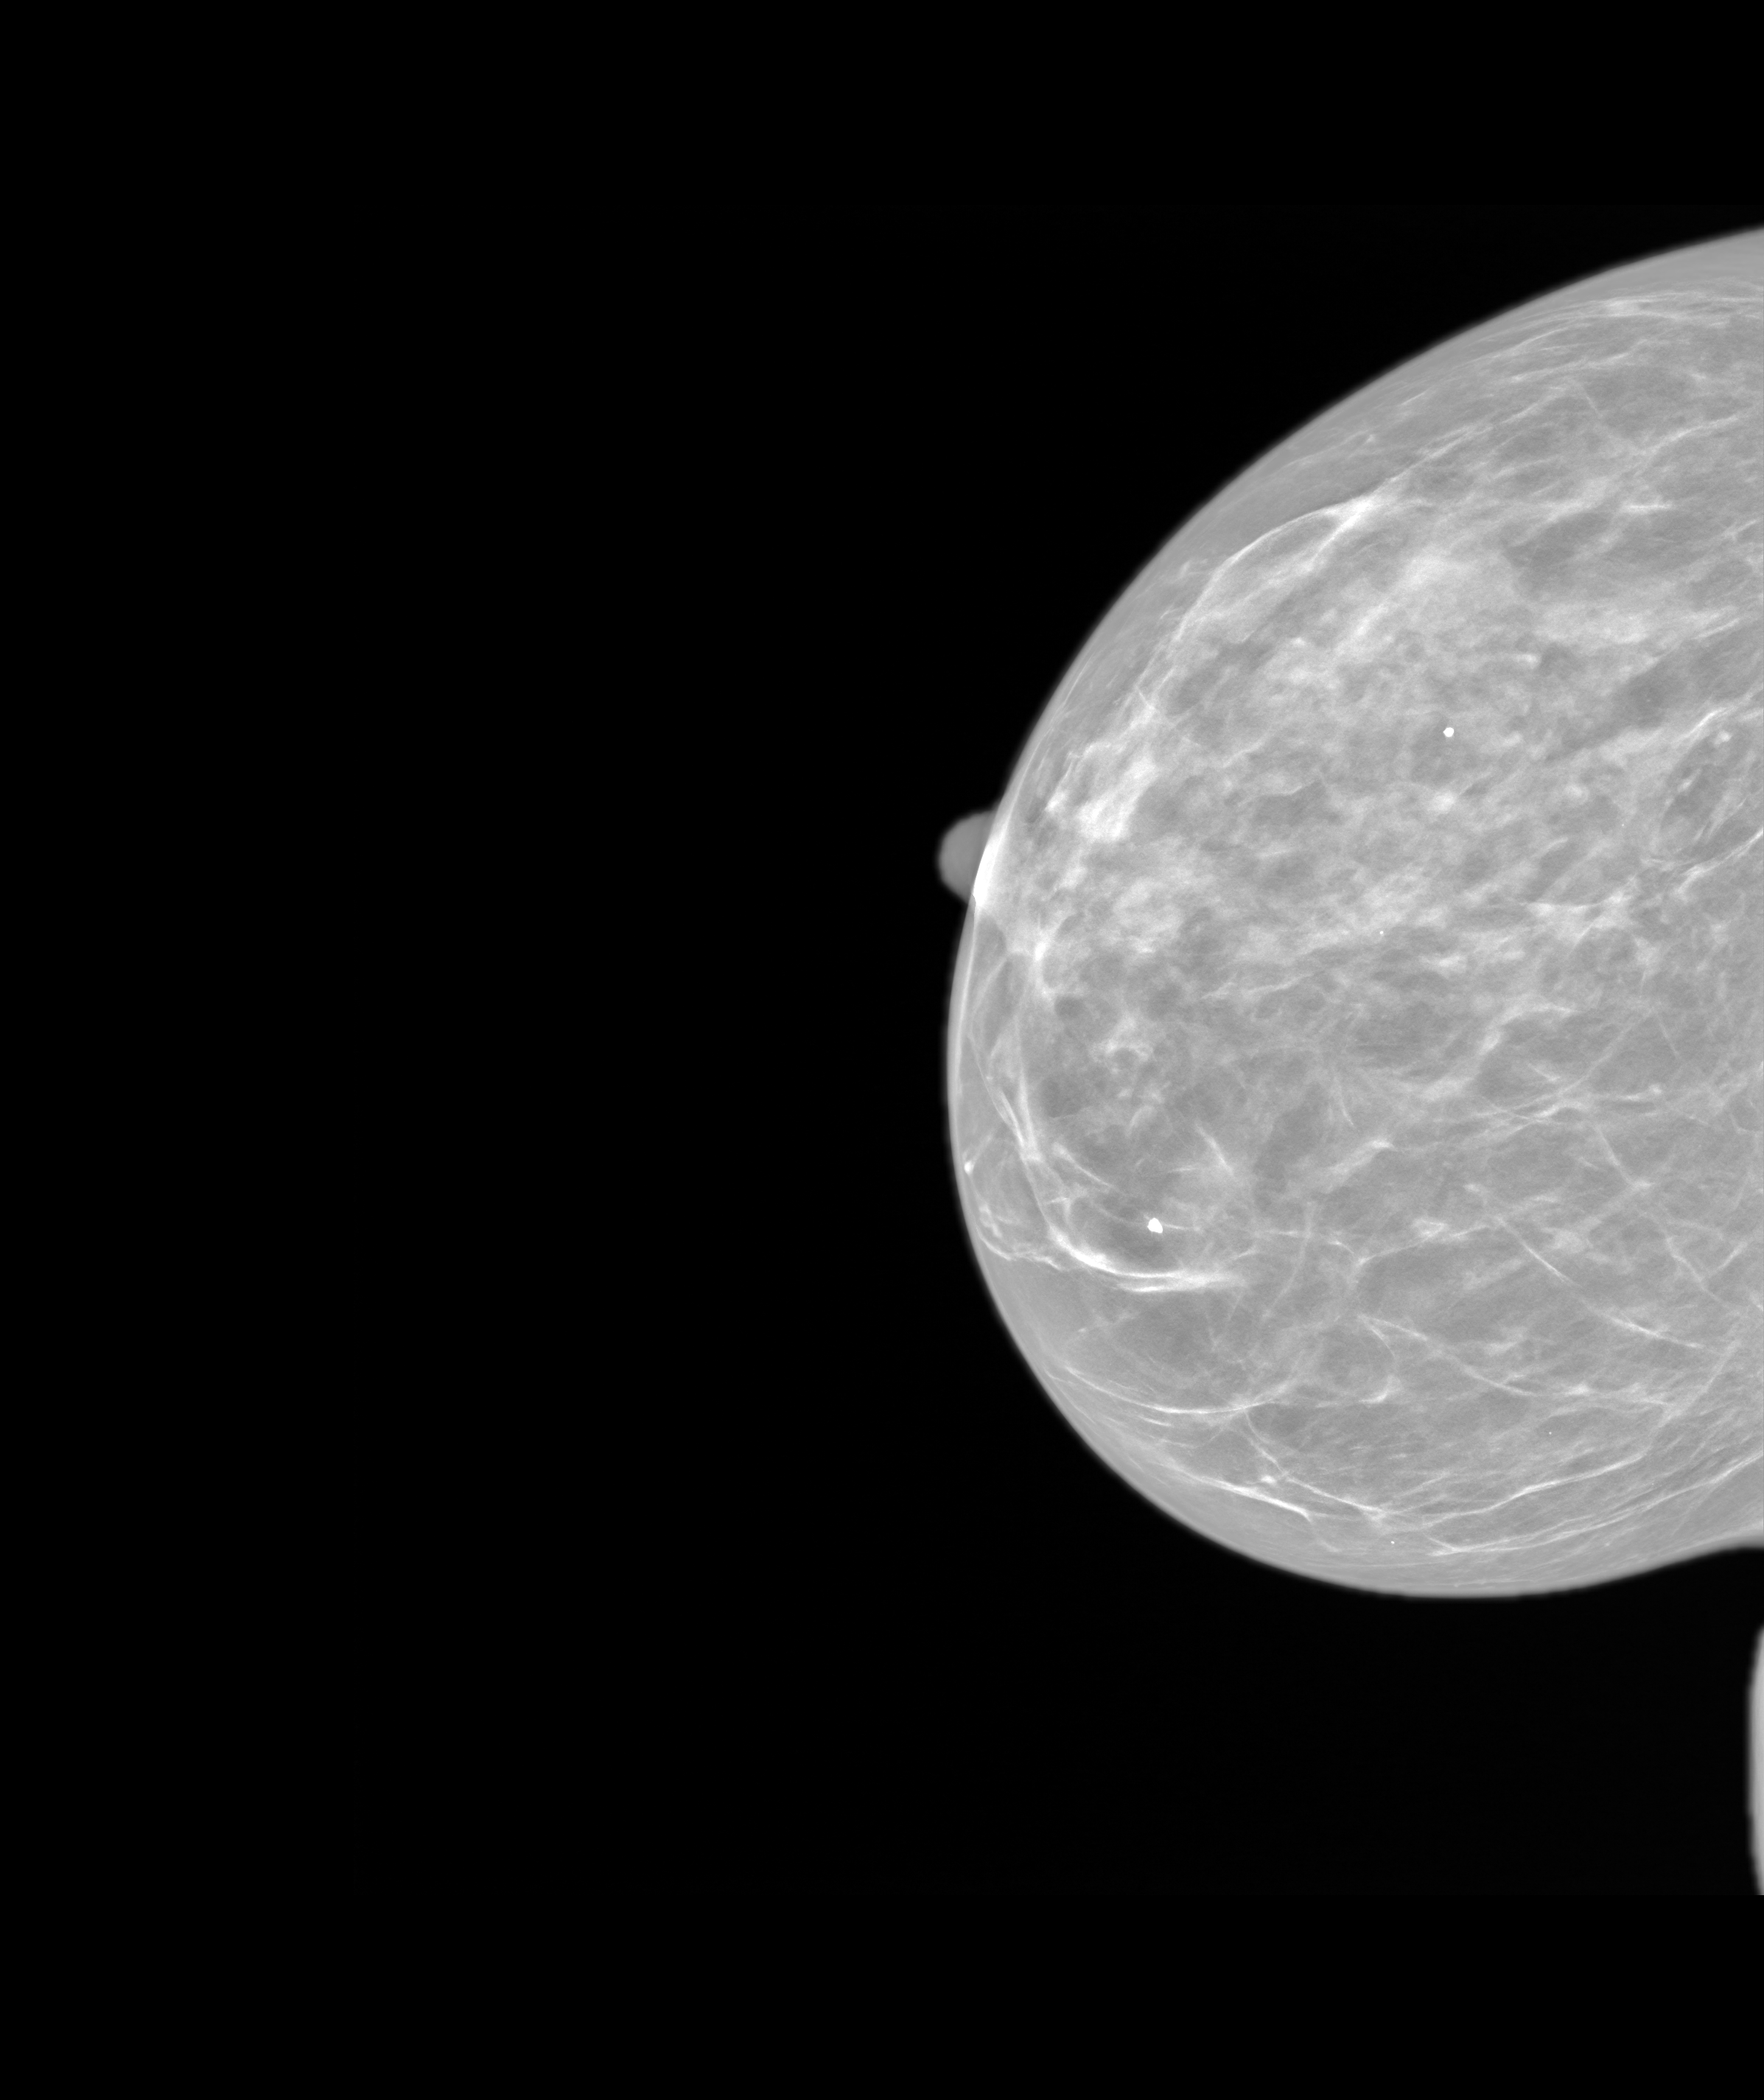
Screening examination. Female patient, age 57 years.
Image type: synthesized 2-D view from tomosynthesis. Breast: right. Projection: CC view.